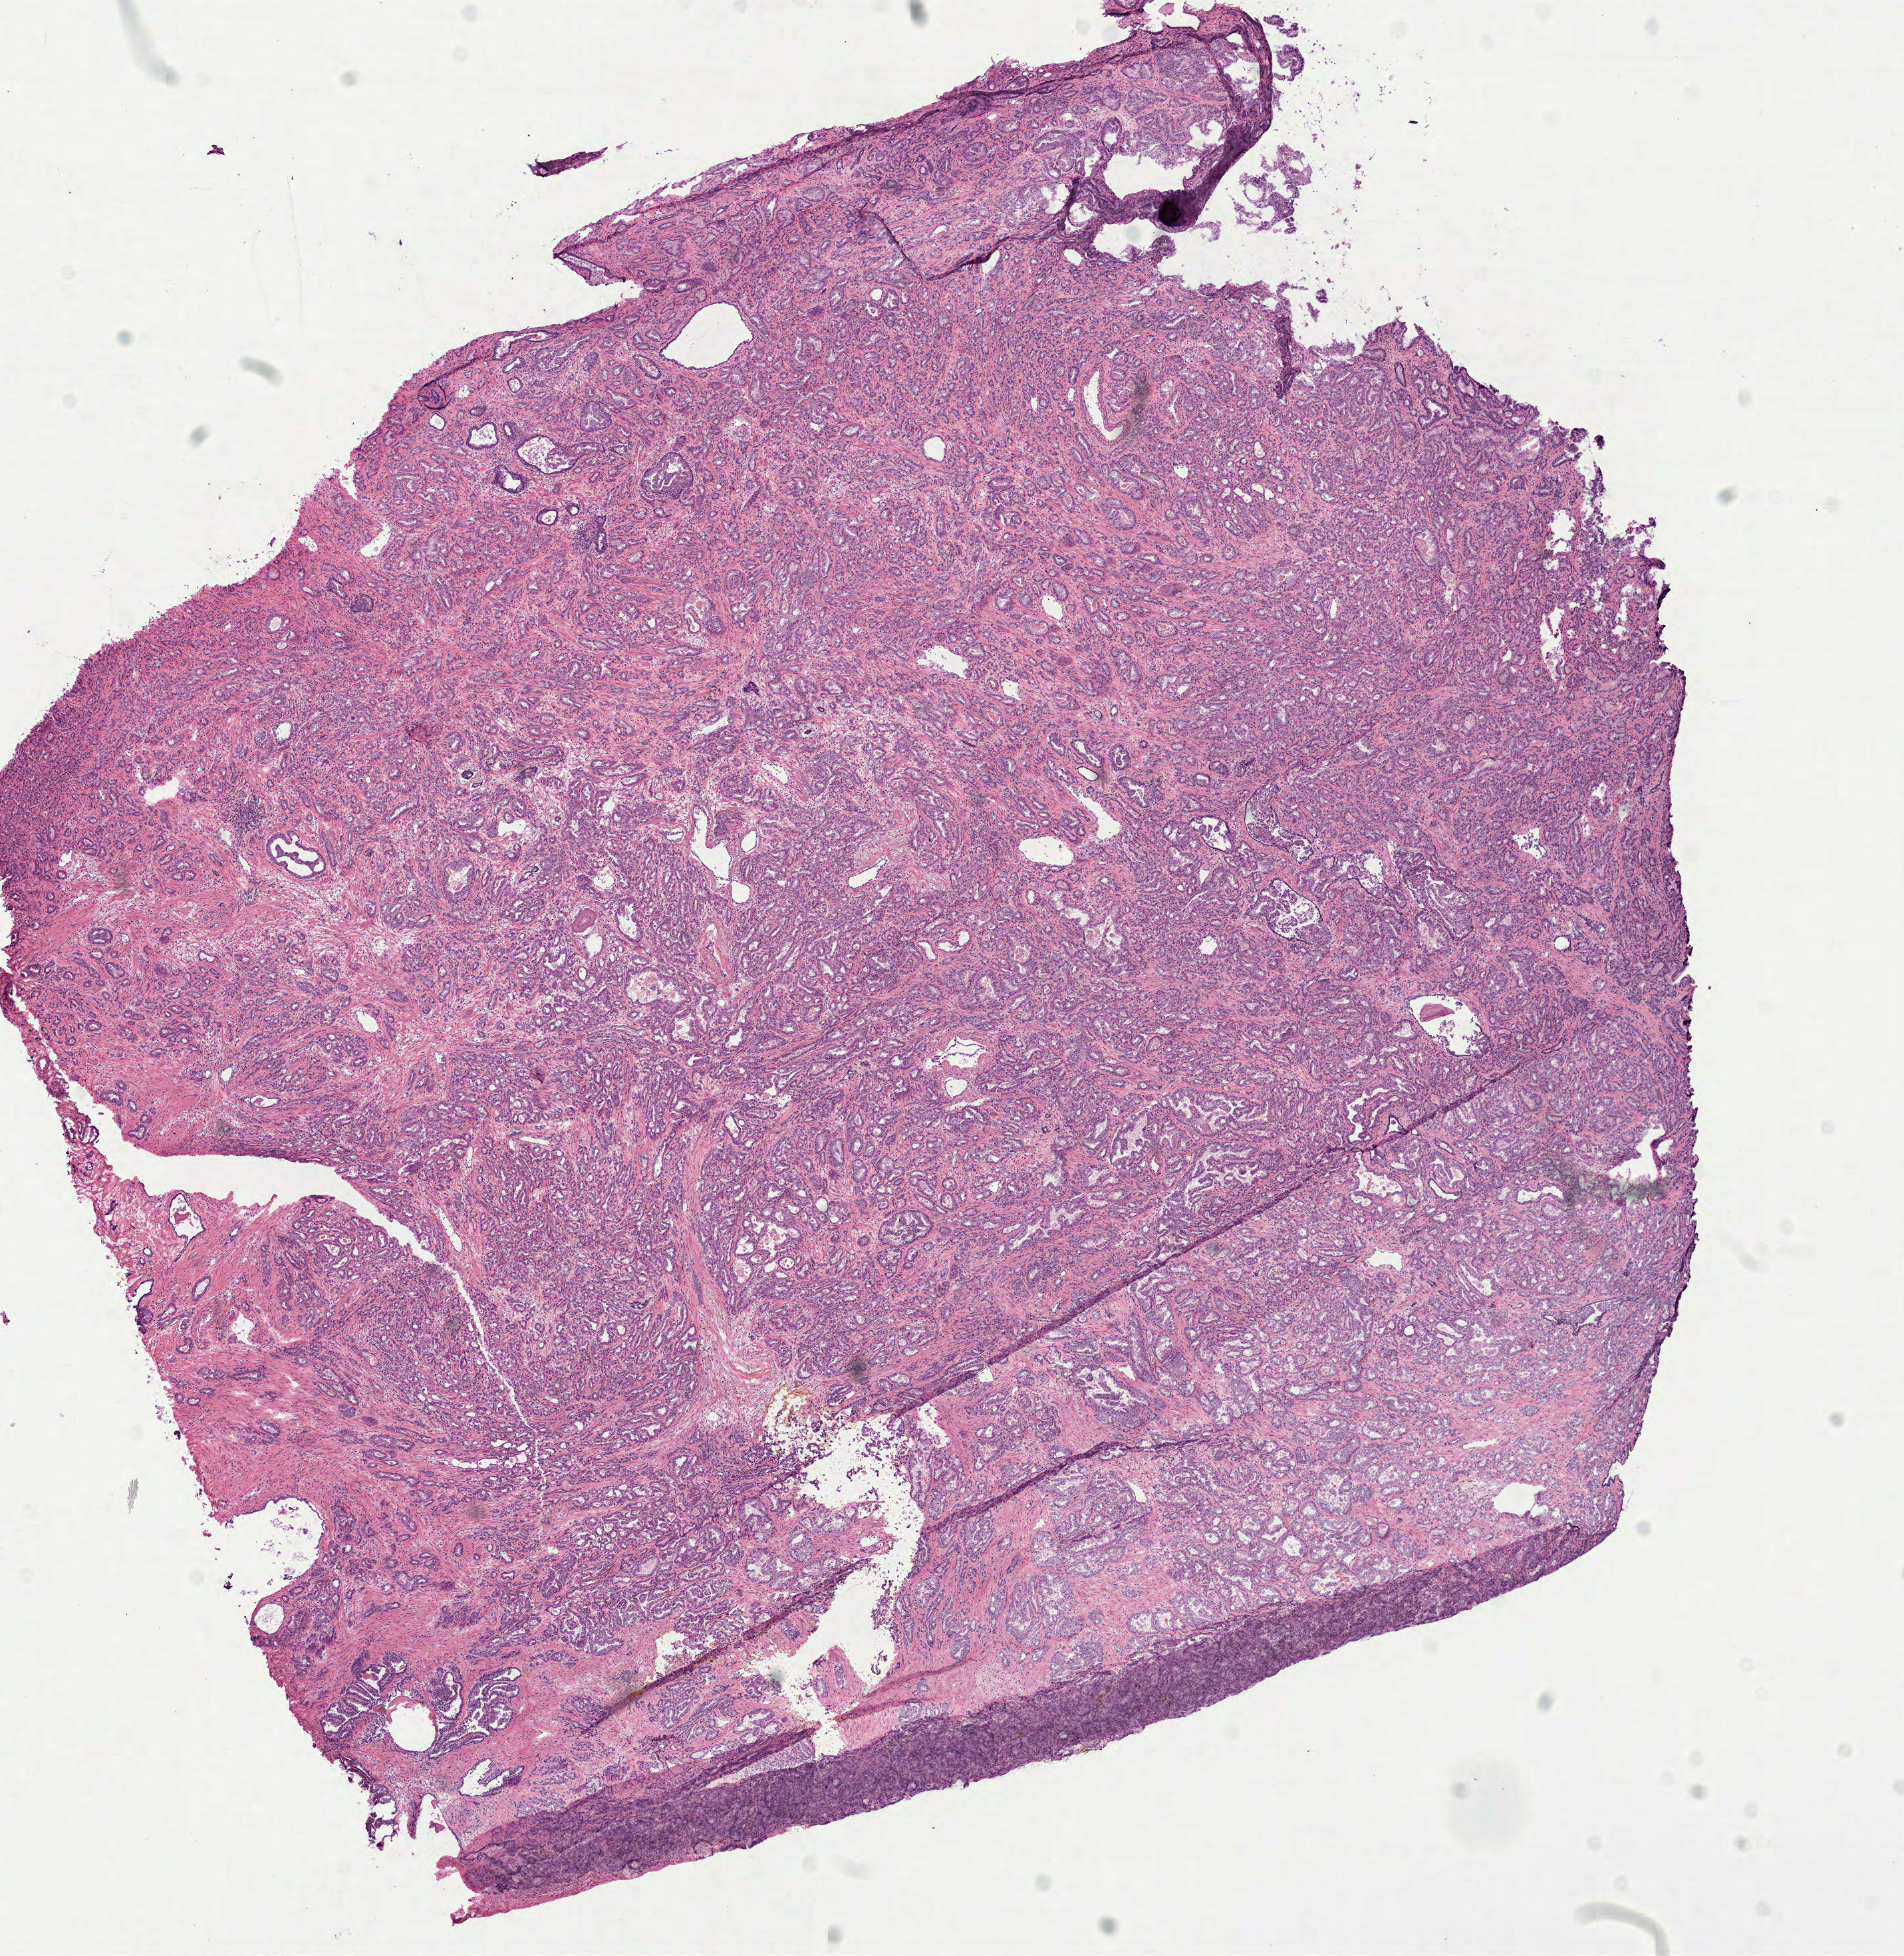
Digitized H&E-stained tissue section (whole slide) — shown as a low-resolution overview of the whole scanned area (about 11.3 x 11.6 mm, acquisition: 40x scan). Frozen section from the top of the tissue portion. Primary tumour sample from the prostate. Male patient; age at initial diagnosis 61 years. Gleason score: 7 (4+3). Composition of this section per pathologist review: tumour cells 75%, tumour nuclei 80%, normal cells 15%, stromal cells 10%, necrosis 0%. Infiltration values recorded for this section: lymphocyte infiltration 2%, monocyte infiltration 0%, neutrophil infiltration 0%.
• diagnosis: Acinar cell carcinoma (prostate gland)
• laterality: left